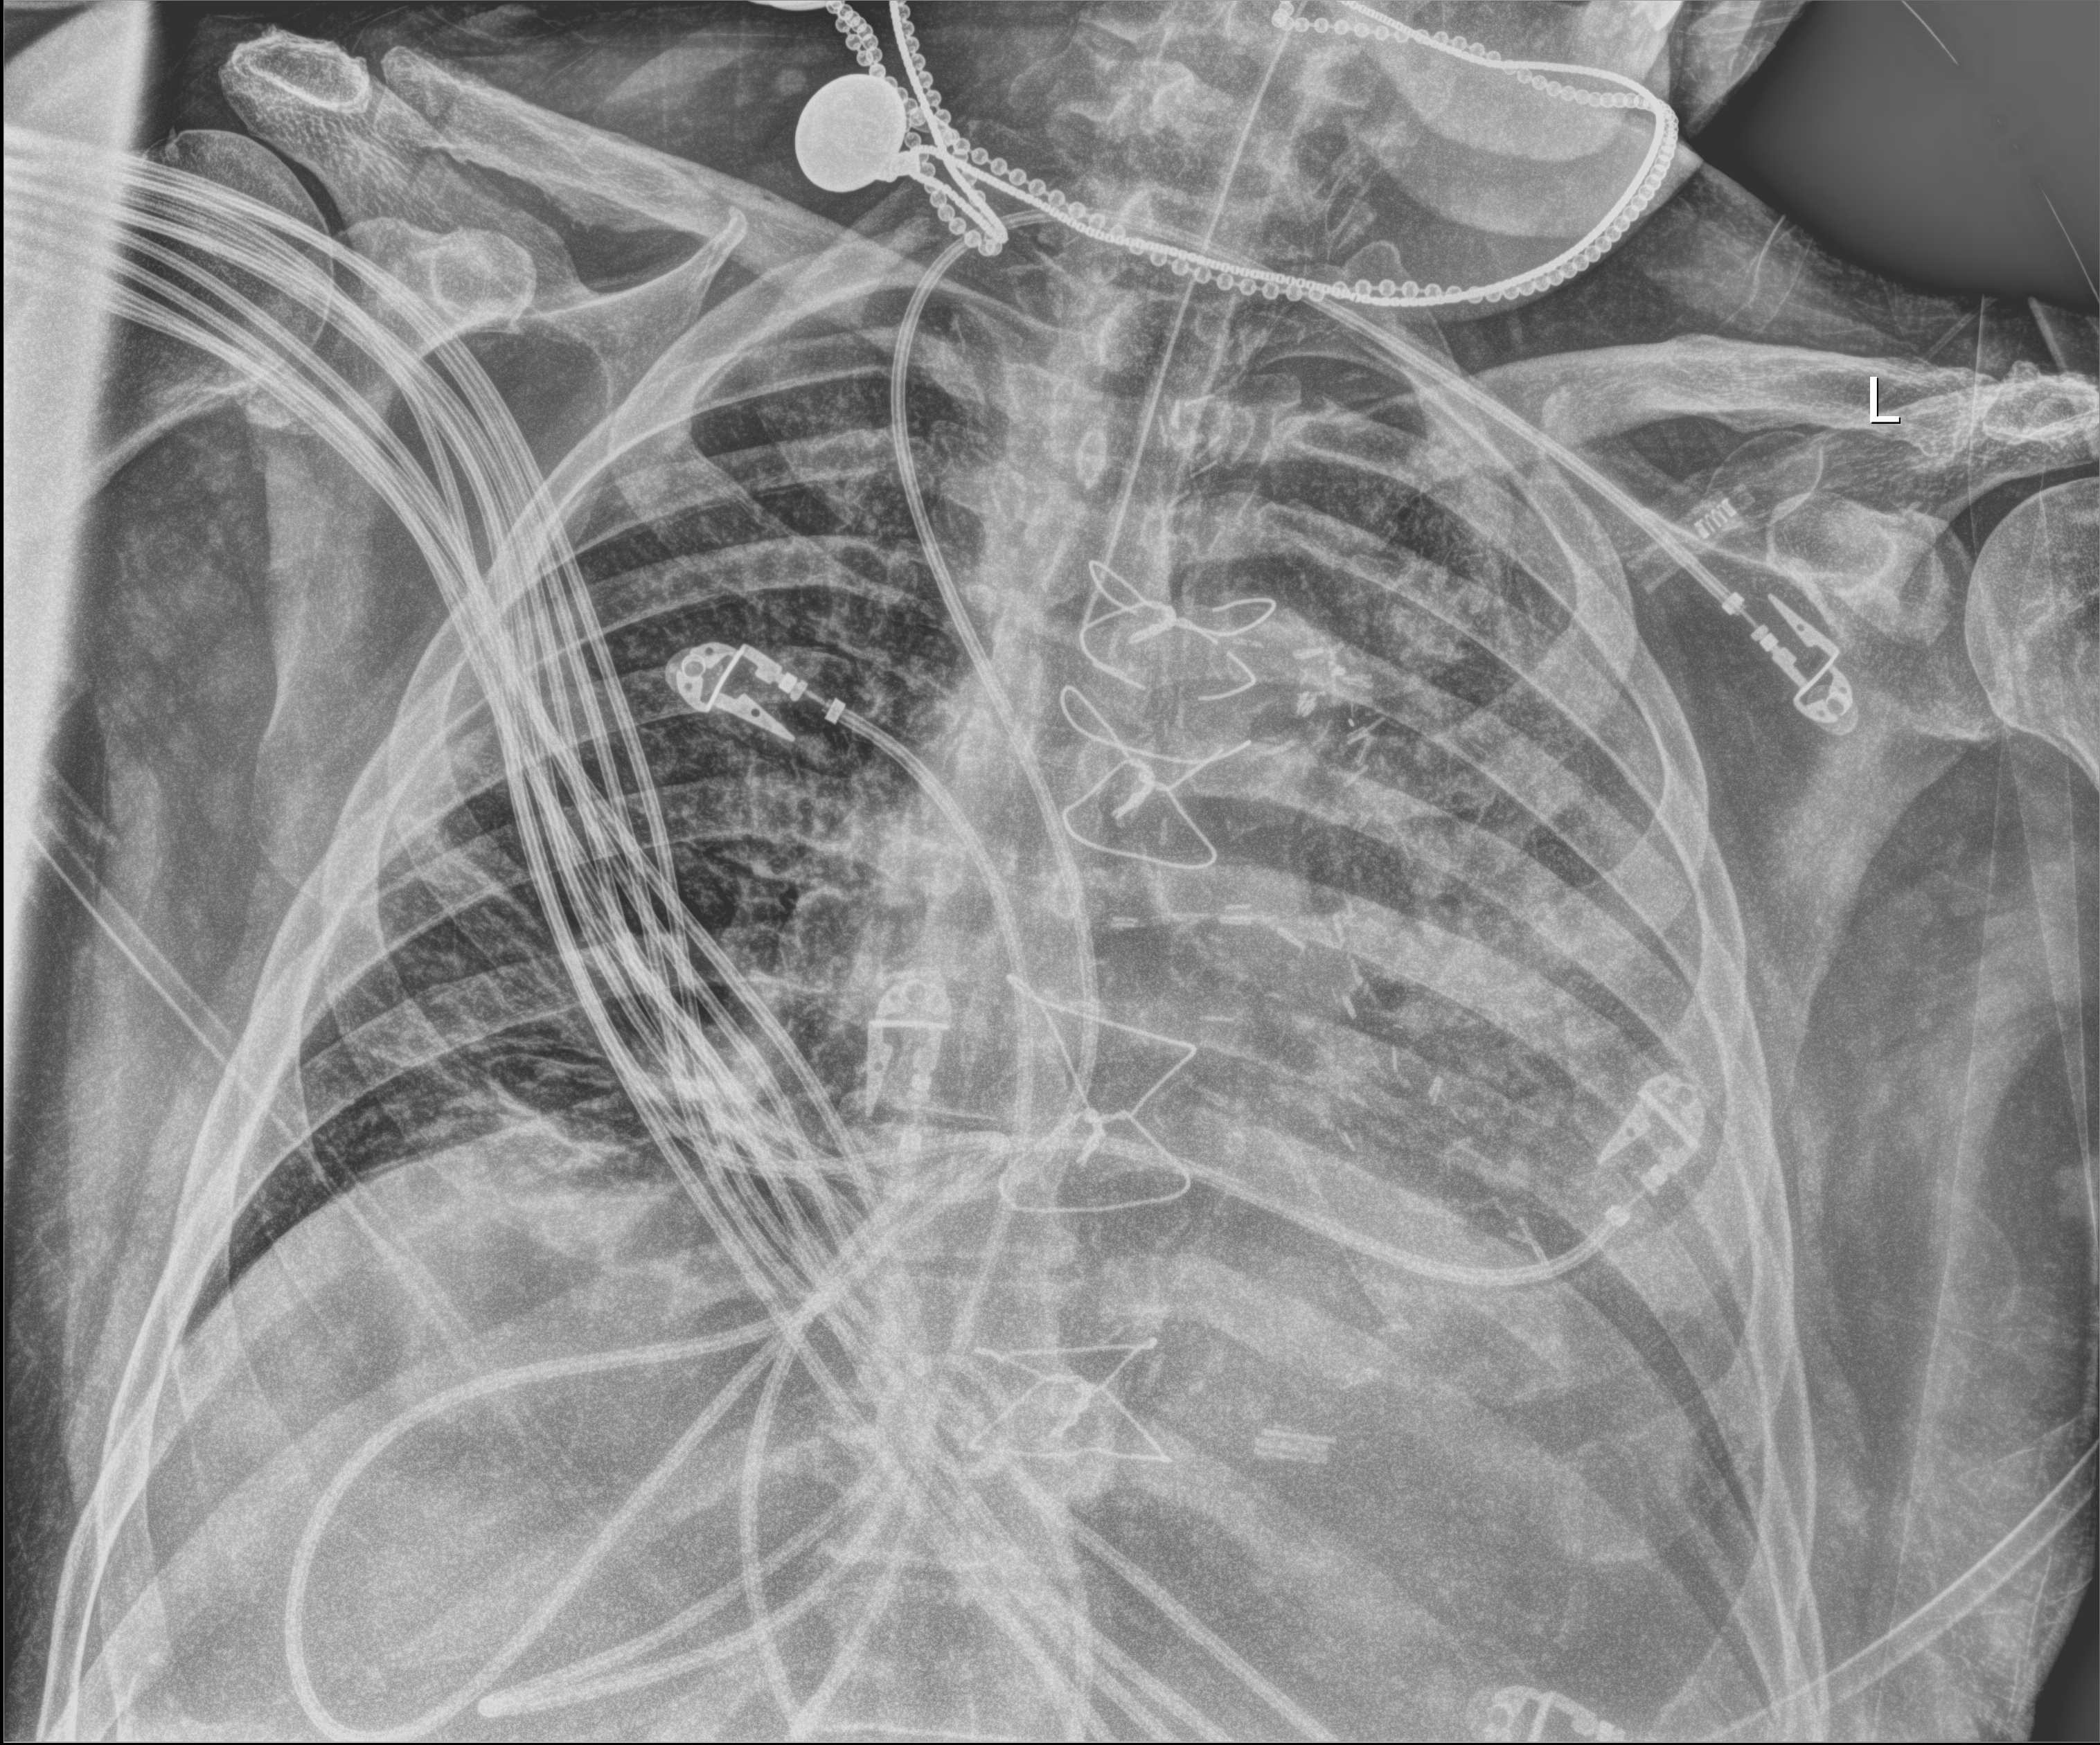
Portable chest radiograph, anteroposterior (AP) projection. Patient hospitalised with COVID-19; male, aged 60–74 years.
Admission-level facts for this patient (not findings on this image; timing relative to this image not recorded): length of hospital stay: 16 days; admitted to intensive care during this hospital stay: yes.